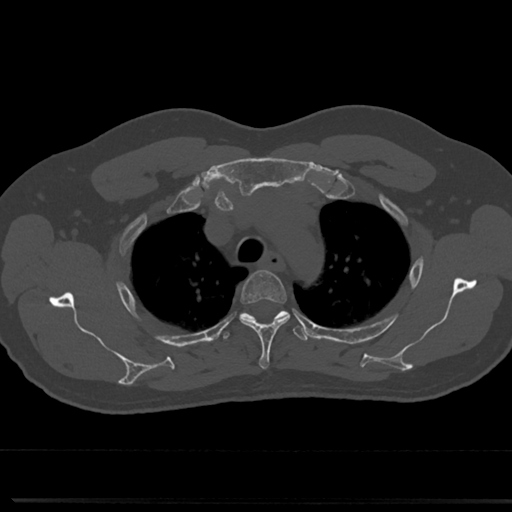
CT including the spine, one axial slice. Position 577 of 817 along the scan axis. Reconstruction kernel Br40s/3. 120 kVp. Bone window (W 1800 / L 400 HU). 0.5 mm slice thickness. 512 × 512 image matrix, field of view 355 × 355 mm. Male patient, age 61 years. Case-level facts recorded for this patient, not image findings: primary cancer: prostate.
Annotated regions visible in this slice (semi-automatically segmented with operator editing):
- T3 vertebra: bounding box [x1, y1, x2, y2] px = [238, 271, 289, 370]
- T4 vertebra: [221, 308, 309, 344]